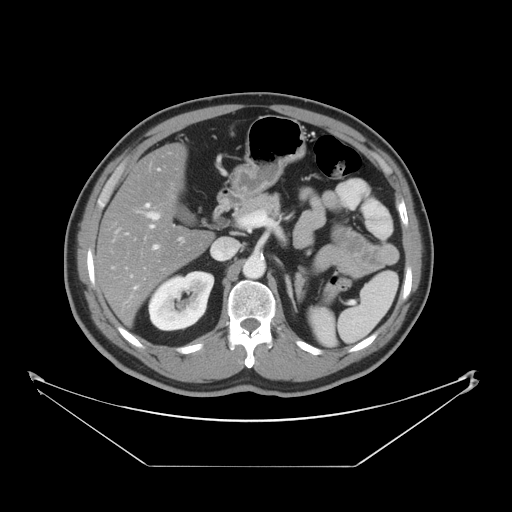
Contrast-enhanced abdominal CT, one axial slice. Slice 24 of 46 in the series (ordered by position). Reconstruction kernel STANDARD. Intravenous contrast given. Soft-tissue window (W 400 / L 40 HU). 5 mm slice thickness. 512 × 512 image matrix, field of view 465 × 465 mm. Male patient, age 57 years. From the clinical record (not read from this slice): diagnosis: colorectal cancer liver metastases, imaged before liver resection; multiple liver metastases: no; largest metastasis: 3.3 cm; disease in both lobes: no.
Annotated regions visible in this slice (outlined manually by an expert reader):
- hepatic veins: bounding box [x1, y1, x2, y2] px = [145, 211, 161, 221]
- liver: [97, 145, 211, 326]
- planned liver remnant (the part of the liver to remain after resection): [97, 145, 212, 326]
- portal vein (with intrahepatic branches): [146, 204, 249, 249]